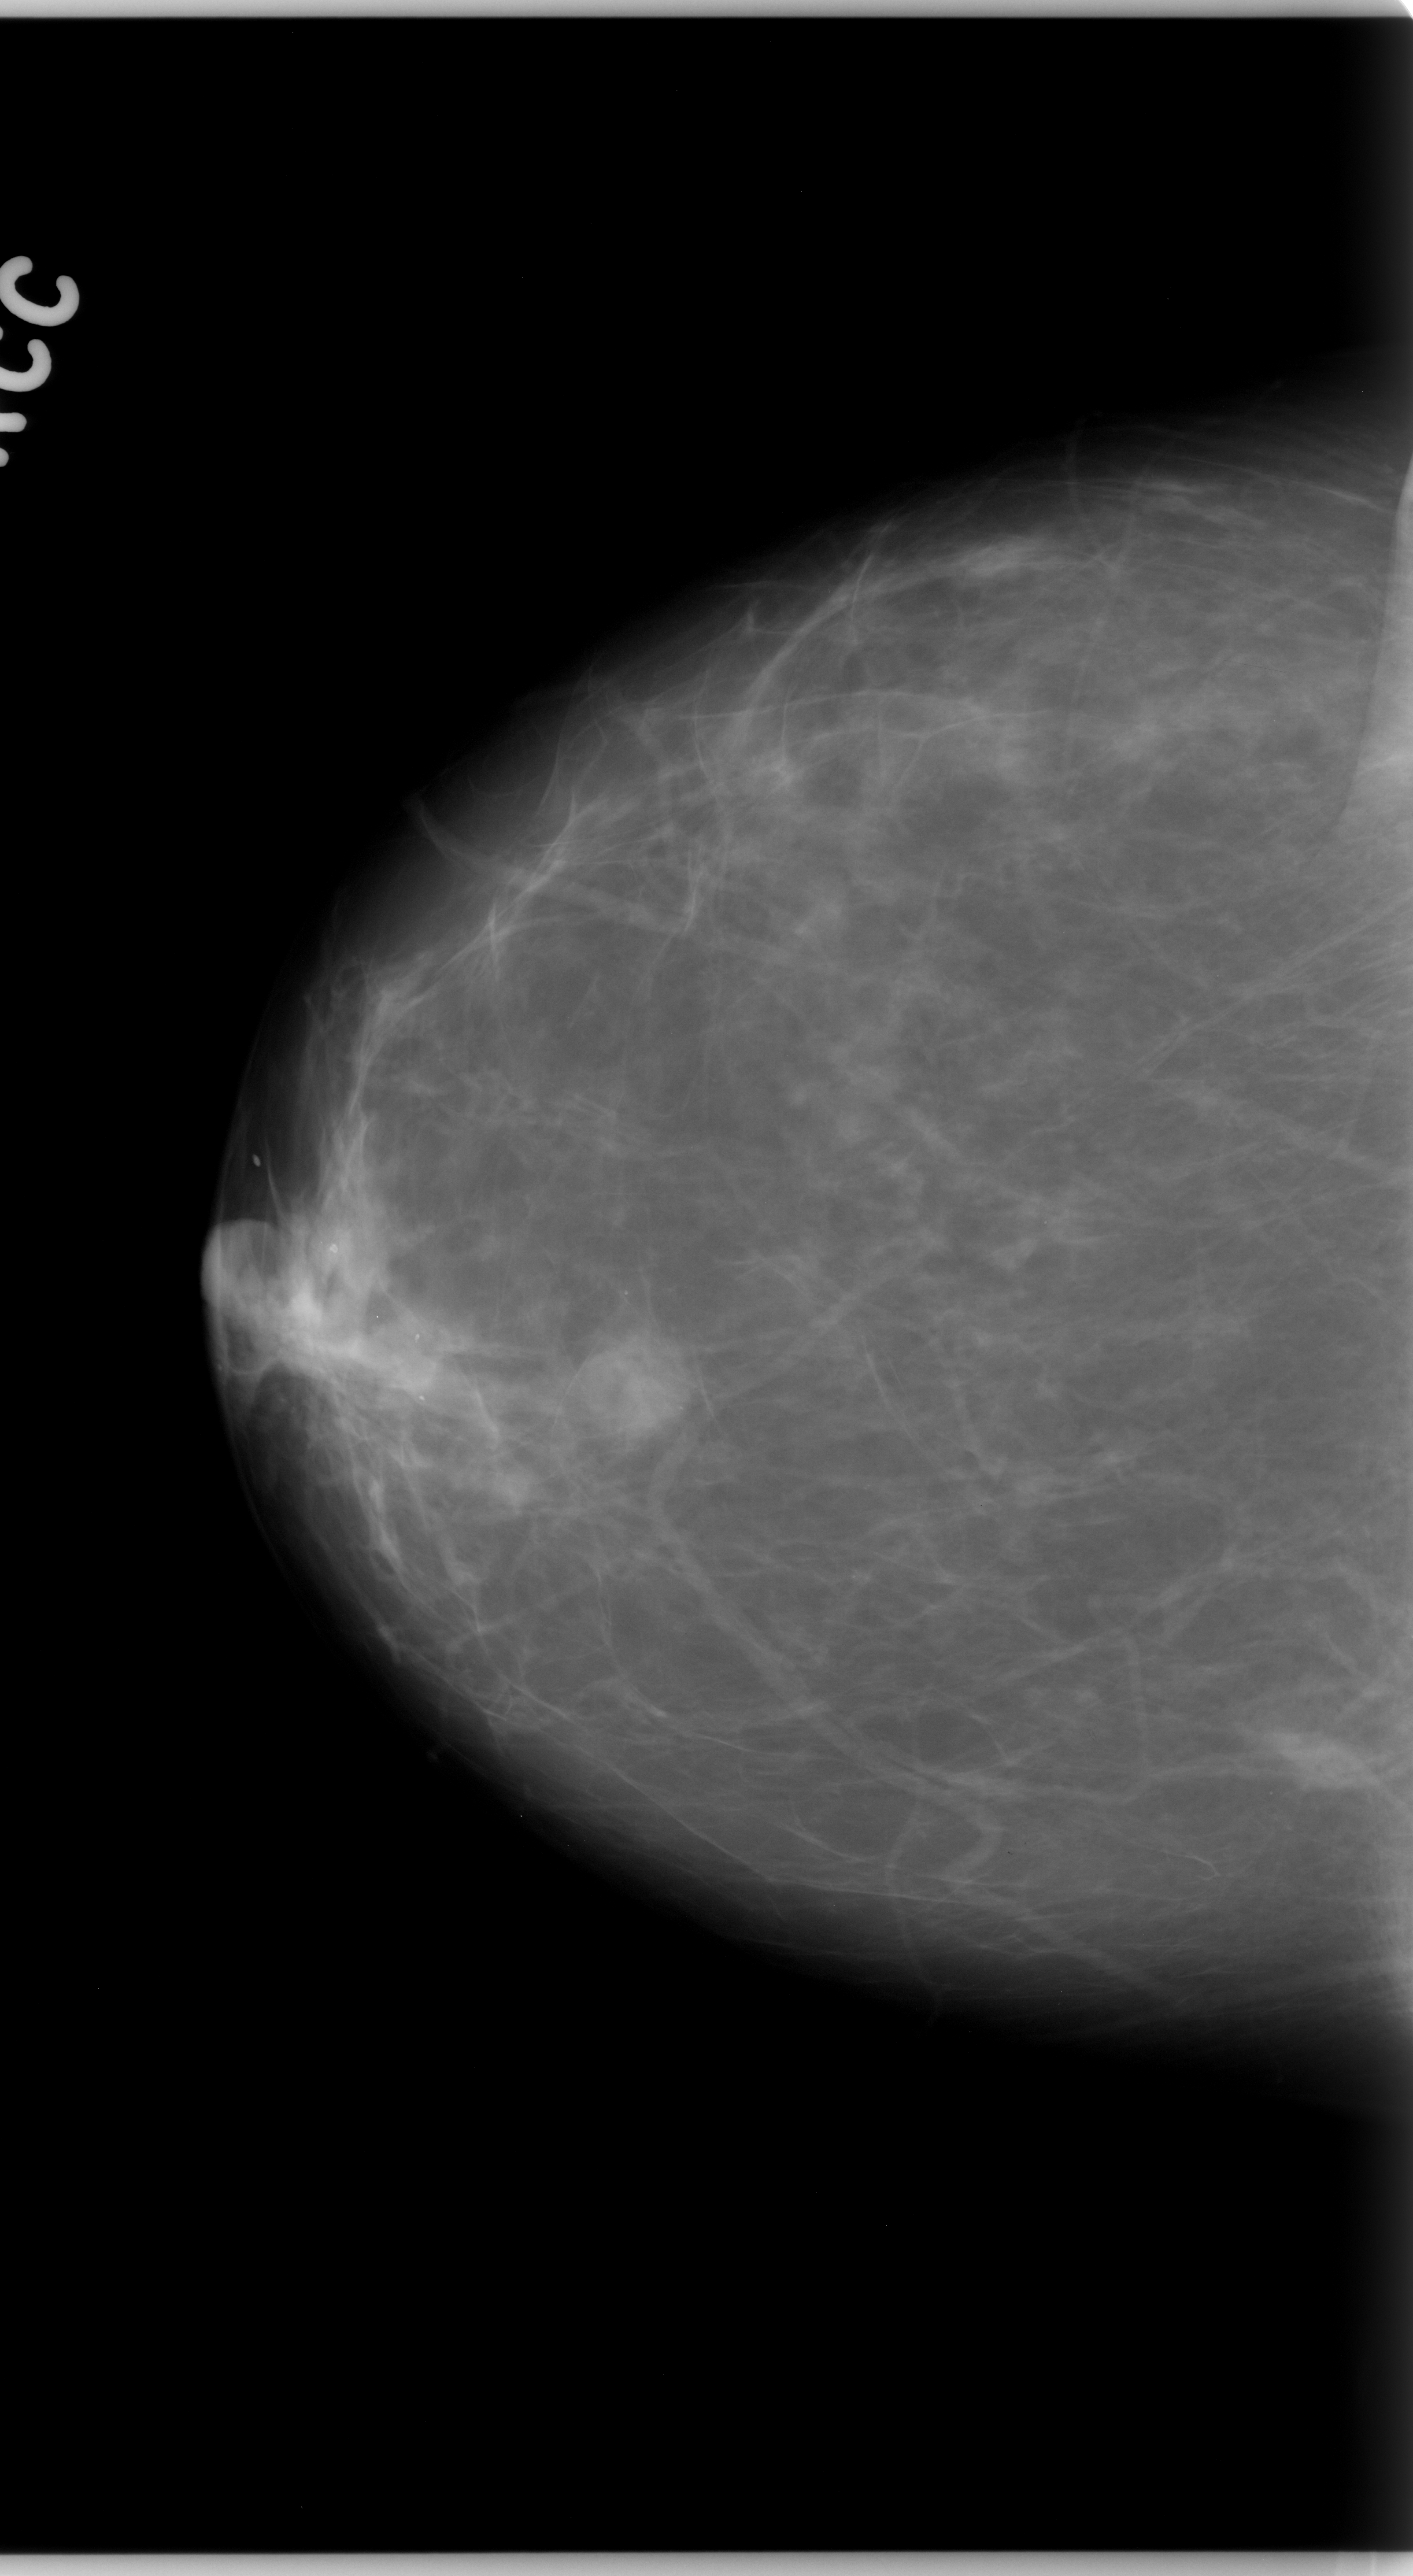
Digitized screen-film mammogram; right breast; craniocaudal (CC) view; breast composition: almost entirely fatty (BI-RADS density category 1 of 4); 1413 × 2576 image matrix.
Expert-marked regions of interest on this film, with their recorded descriptors:
- mass, shape round, margins microlobulated; BI-RADS assessment category 4; subtlety rating 5 on a 1 (subtle) to 5 (obvious) scale; pathology (as recorded): malignant: bounding box <556,1313,718,1463> (left, top, right, bottom; pixels)